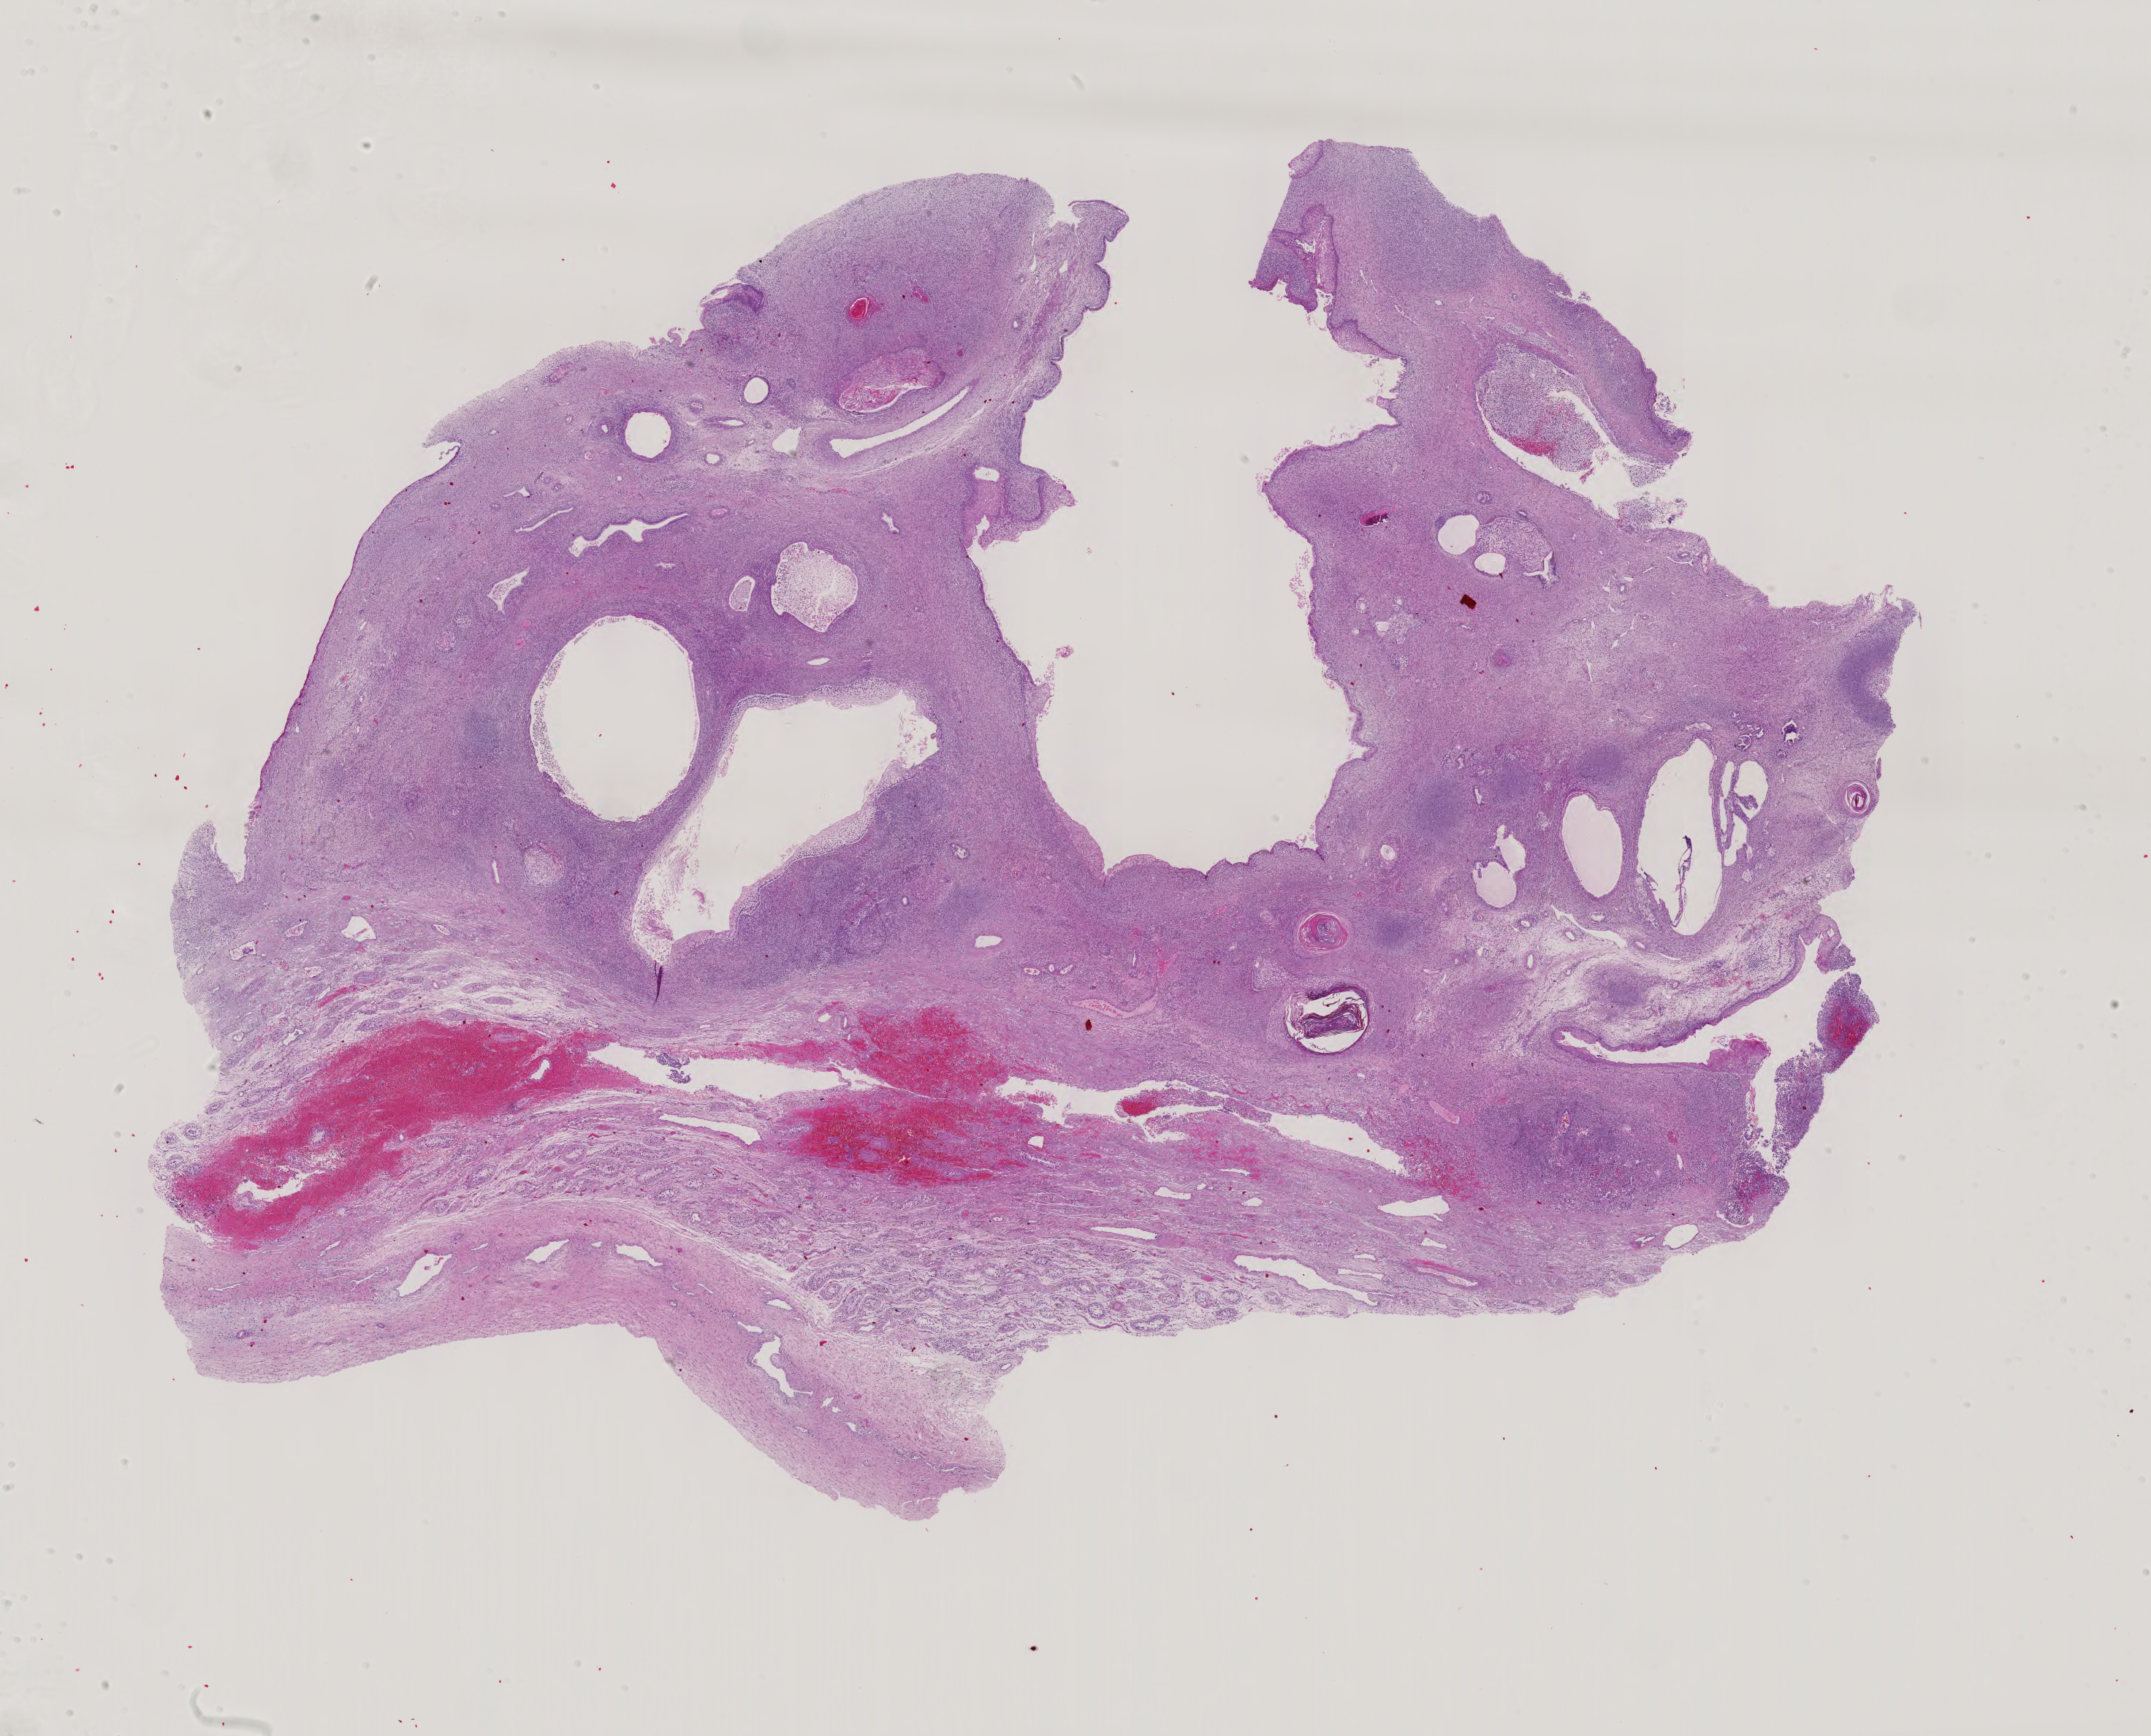
Whole-slide histology image, Hematoxylin and eosin (H&E) stained, a low-resolution overview of the entire scanned area, about 21.5 x 17.3 mm (acquisition: 40x scan). Patient sex: male.
• specimen: formalin-fixed paraffin-embedded (FFPE) diagnostic section; testis, primary tumour sample